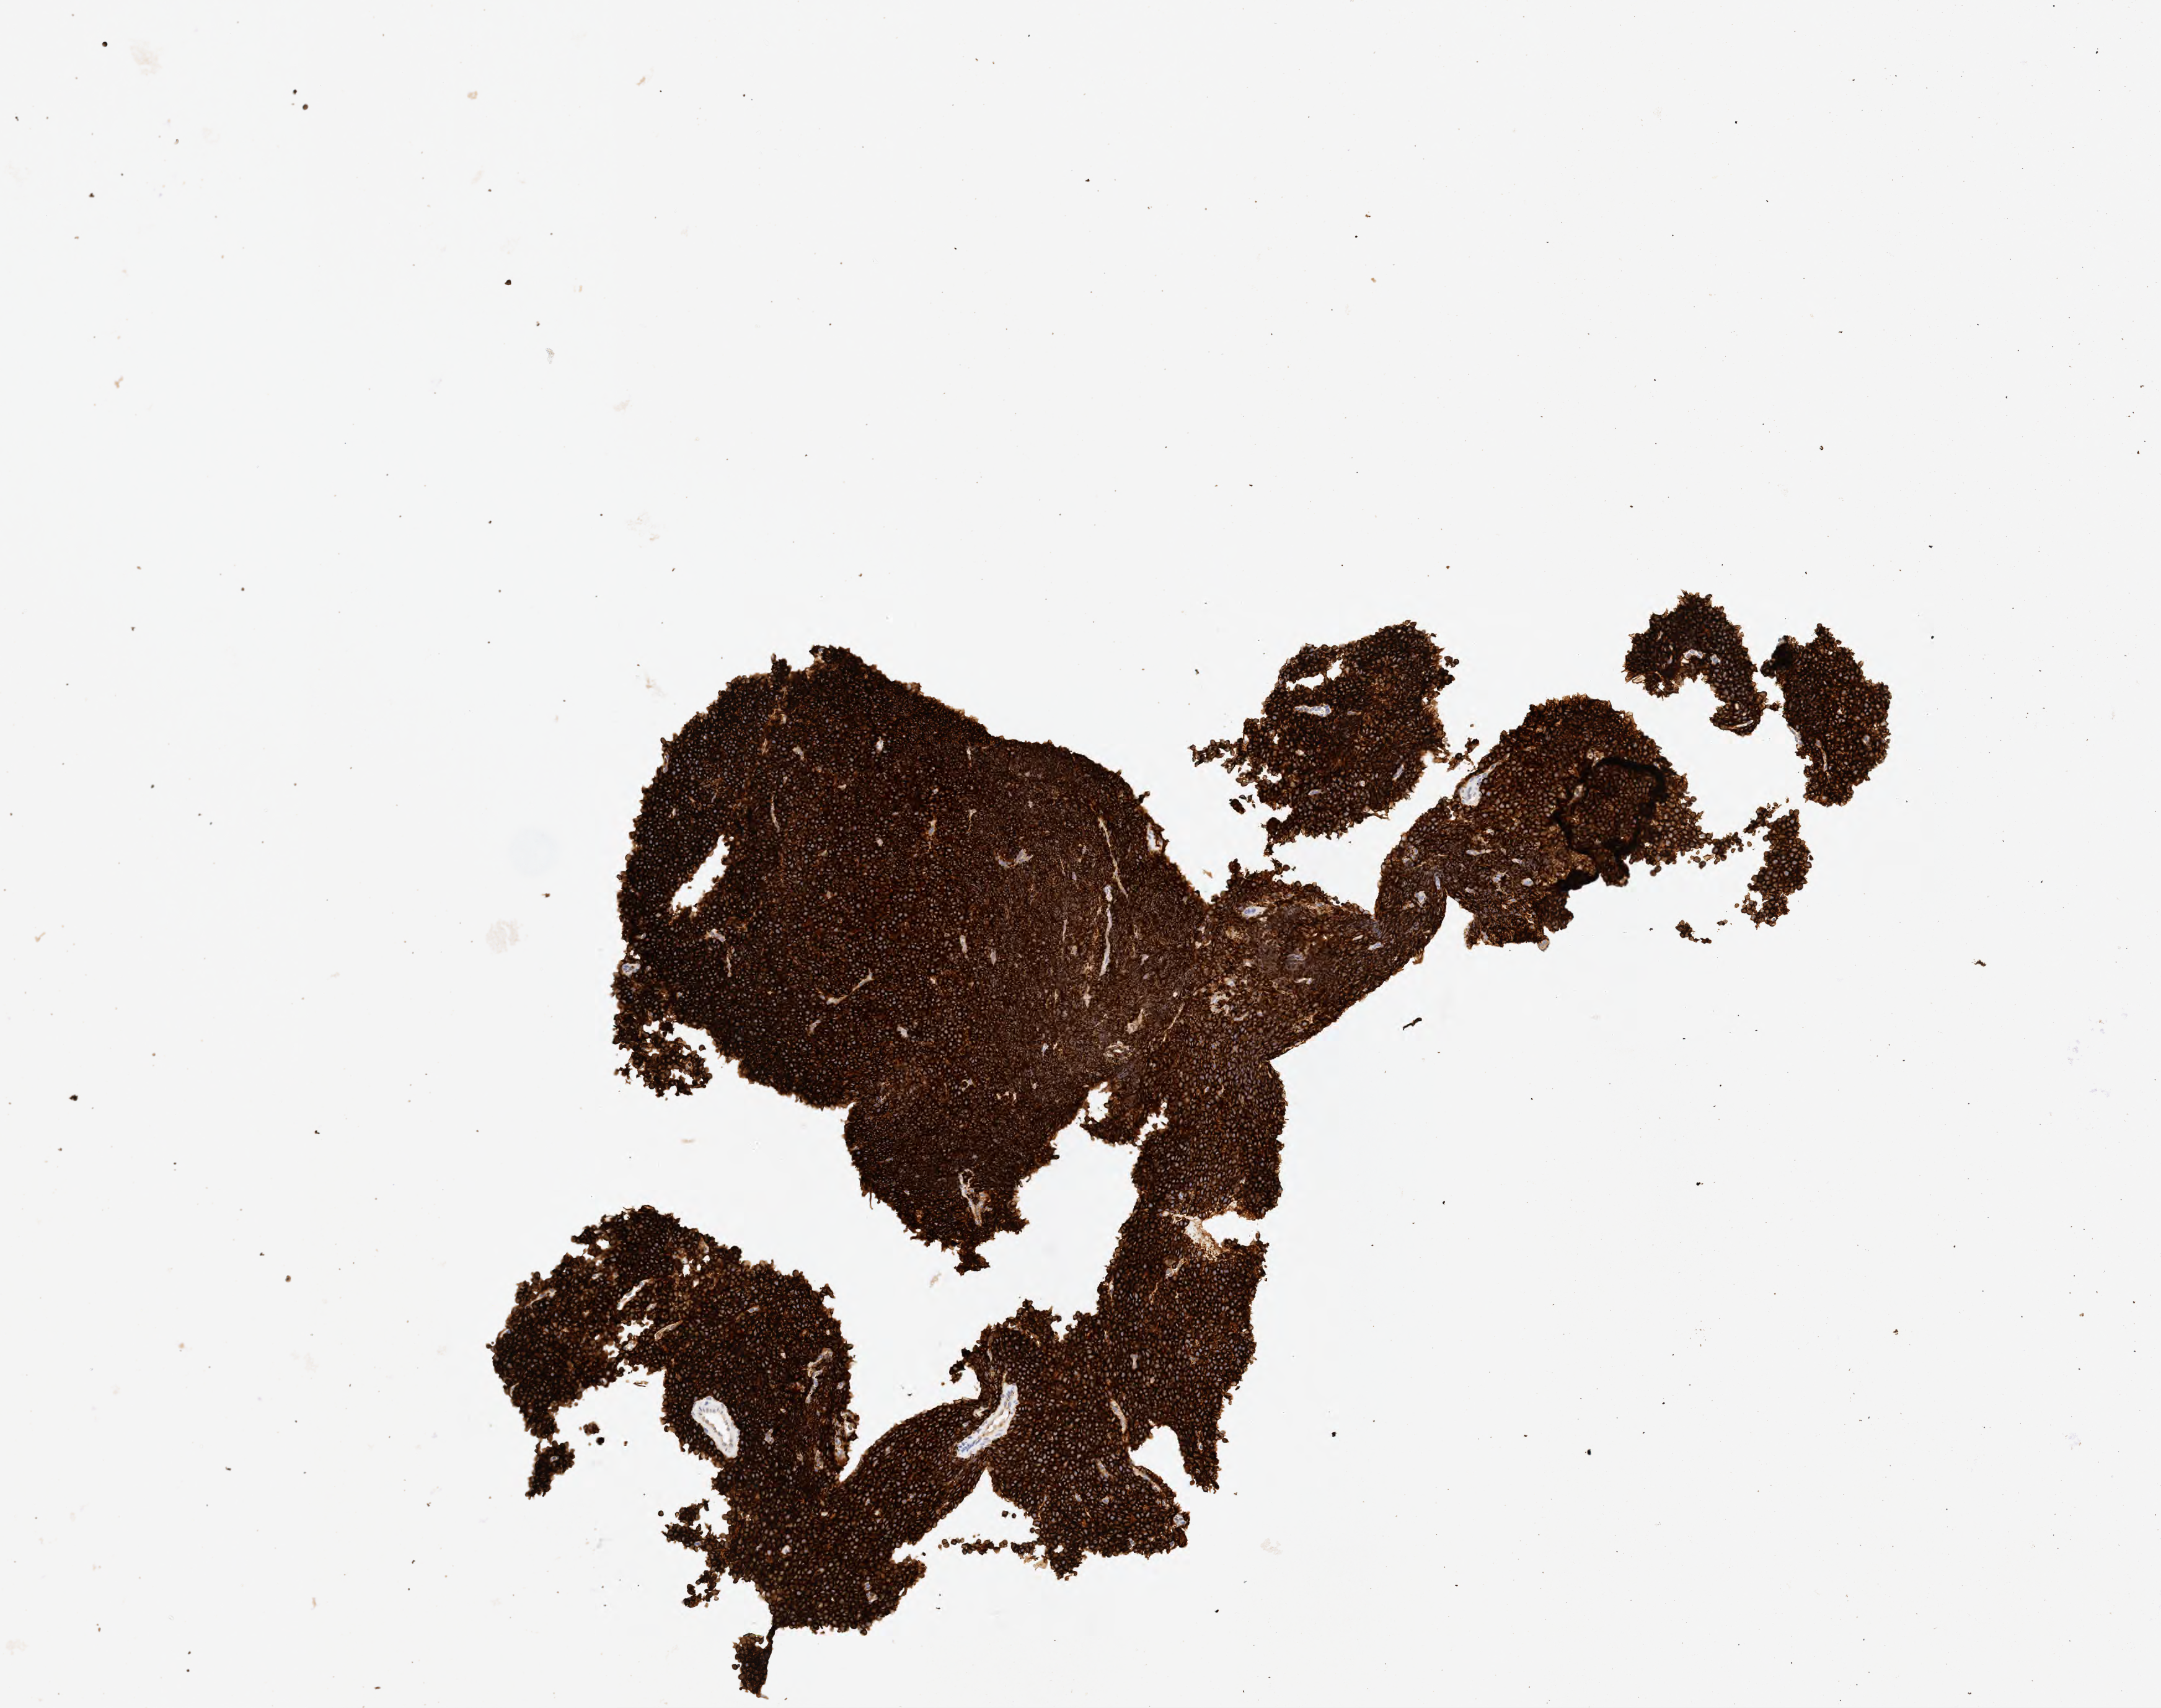
Immunohistochemistry (IHC) whole-slide image stained for CD20, shown as a low-resolution overview of the whole scanned area (about 3.5 x 2.8 mm). Tumor tissue. Male, age 8 years at initial diagnosis.
Diagnosis: Burkitt lymphoma, NOS.